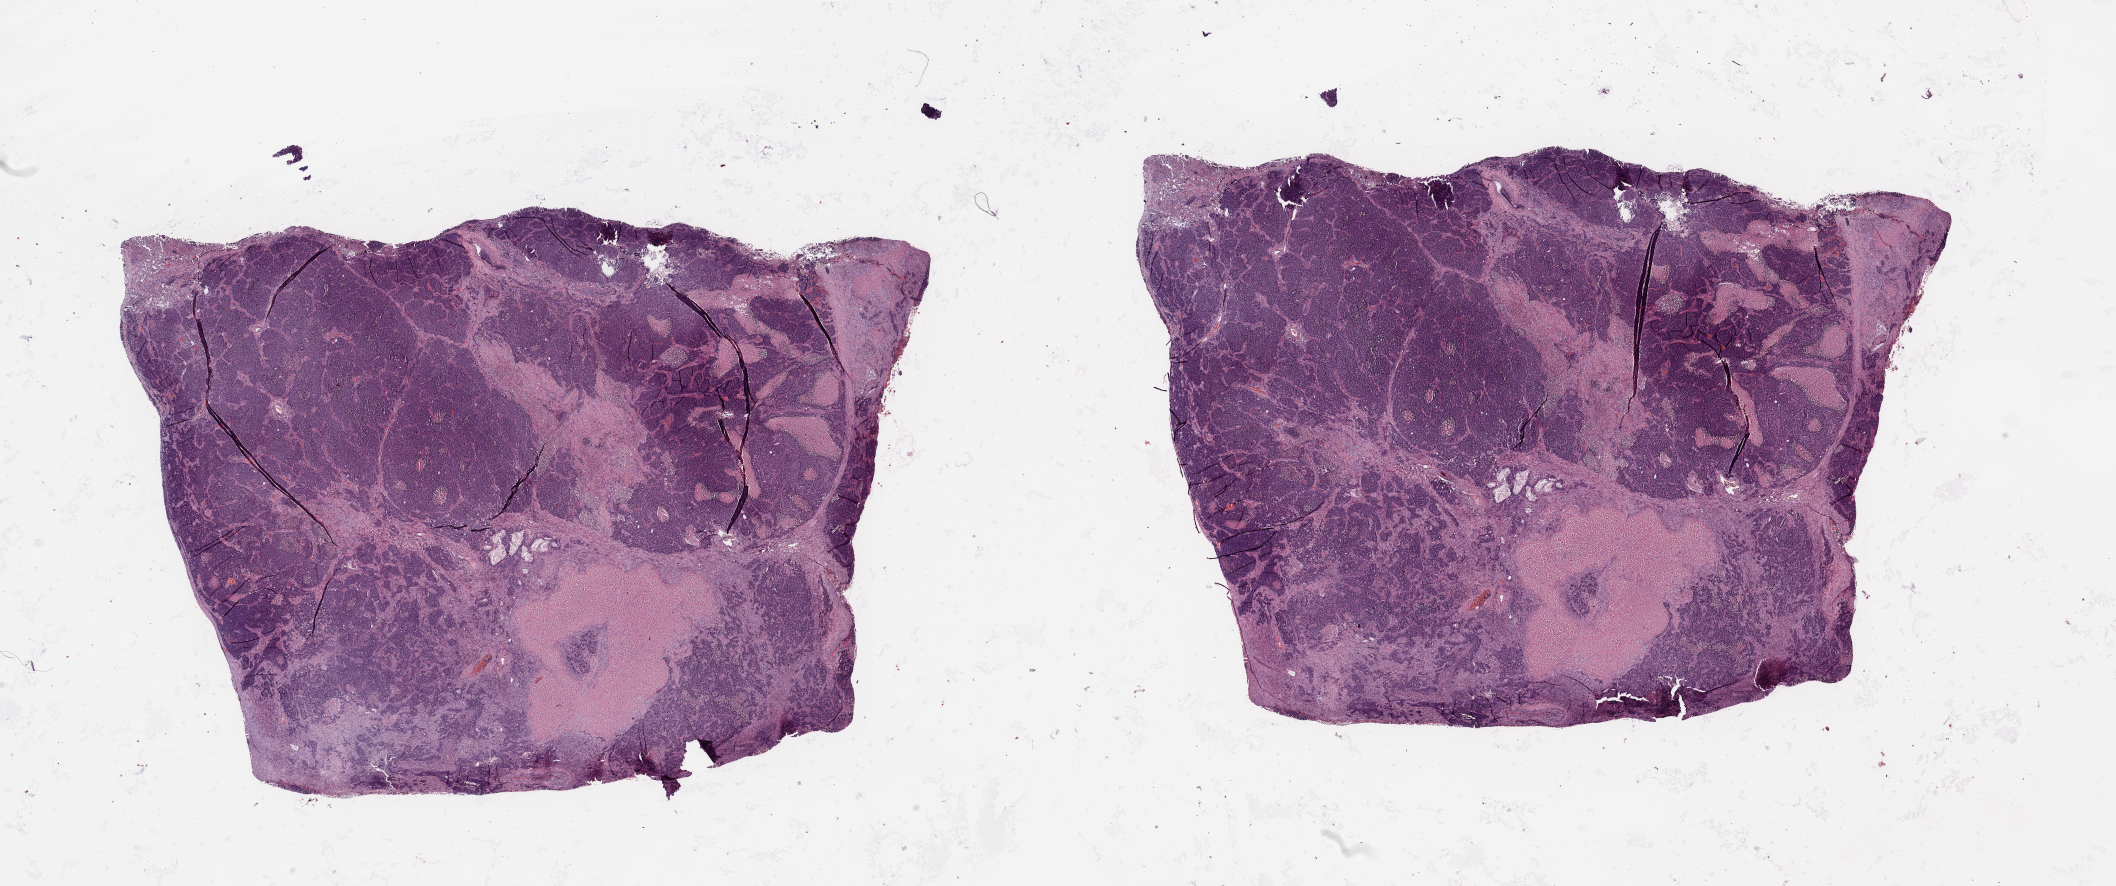
Whole-slide histology image, H&E, a low-resolution overview of the entire scanned area, about 33.5 x 14.0 mm, lung, tumour tissue. Male, 63 y/o.
* primary tumour site (as recorded): left upper lobe
* patient diagnosis (cohort enrolment): squamous cell carcinoma (lung)